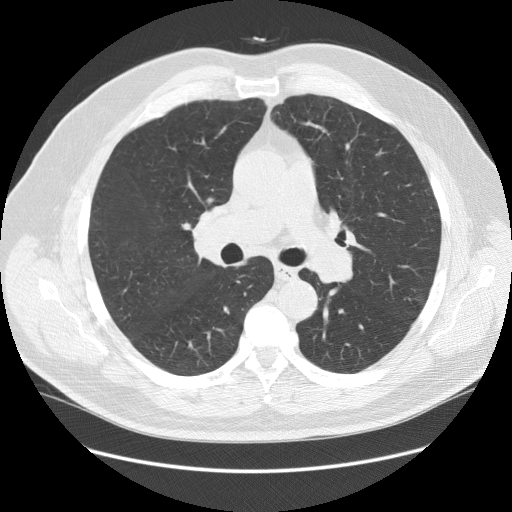
Chest CT (low-dose screening protocol), one axial image, first (baseline) screen, lung window (W 1500 / L -600 HU), 2.5 mm slice thickness, standard (soft-tissue) reconstruction kernel (STANDARD), 120 kVp, slice 57 of 140 in the series. Male participant, aged 64 years at enrolment.
Expert reader's lesion annotation, bounding box <181,195,248,268> (left, top, right, bottom; pixels). The exam's reader record, not a measurement of the box and not confirmed to be the same lesion: non-calcified nodule or mass ≥4 mm, right lower lobe, 7 × 5 mm, smooth margins, soft tissue attenuation. Lung cancer was diagnosed 456 days after this screen (after the second annual screen): adenocarcinoma, NOS, right upper lobe, poorly differentiated (G3), stage IB (AJCC 6th edition), 37 mm at pathology.